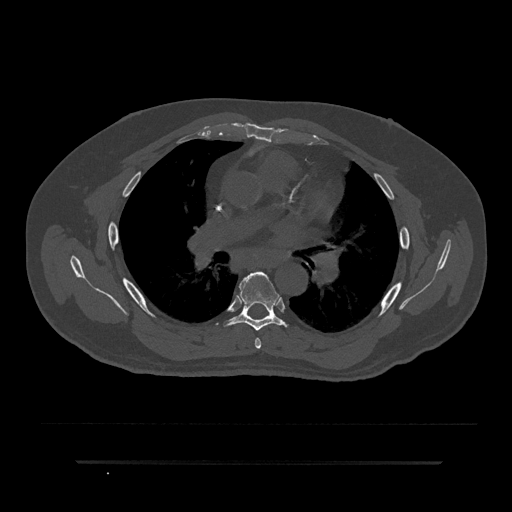
CT including the spine, one axial slice; slice 533 of 797 in the series (ordered by position); reconstruction kernel Br40s/3; bone window (W 1800 / L 400 HU); 0.5 mm slice thickness; 512 × 512 image matrix, field of view 464 × 464 mm. Patient: male, 59 years. From the clinical record (not read from this slice): primary cancer: bile ducts.
Annotated regions visible in this slice (semi-automatically segmented with operator editing):
- T5 vertebra: bounding box (x1, y1, x2, y2) in pixels: (255, 338, 262, 349)
- T6 vertebra: (223, 271, 288, 331)